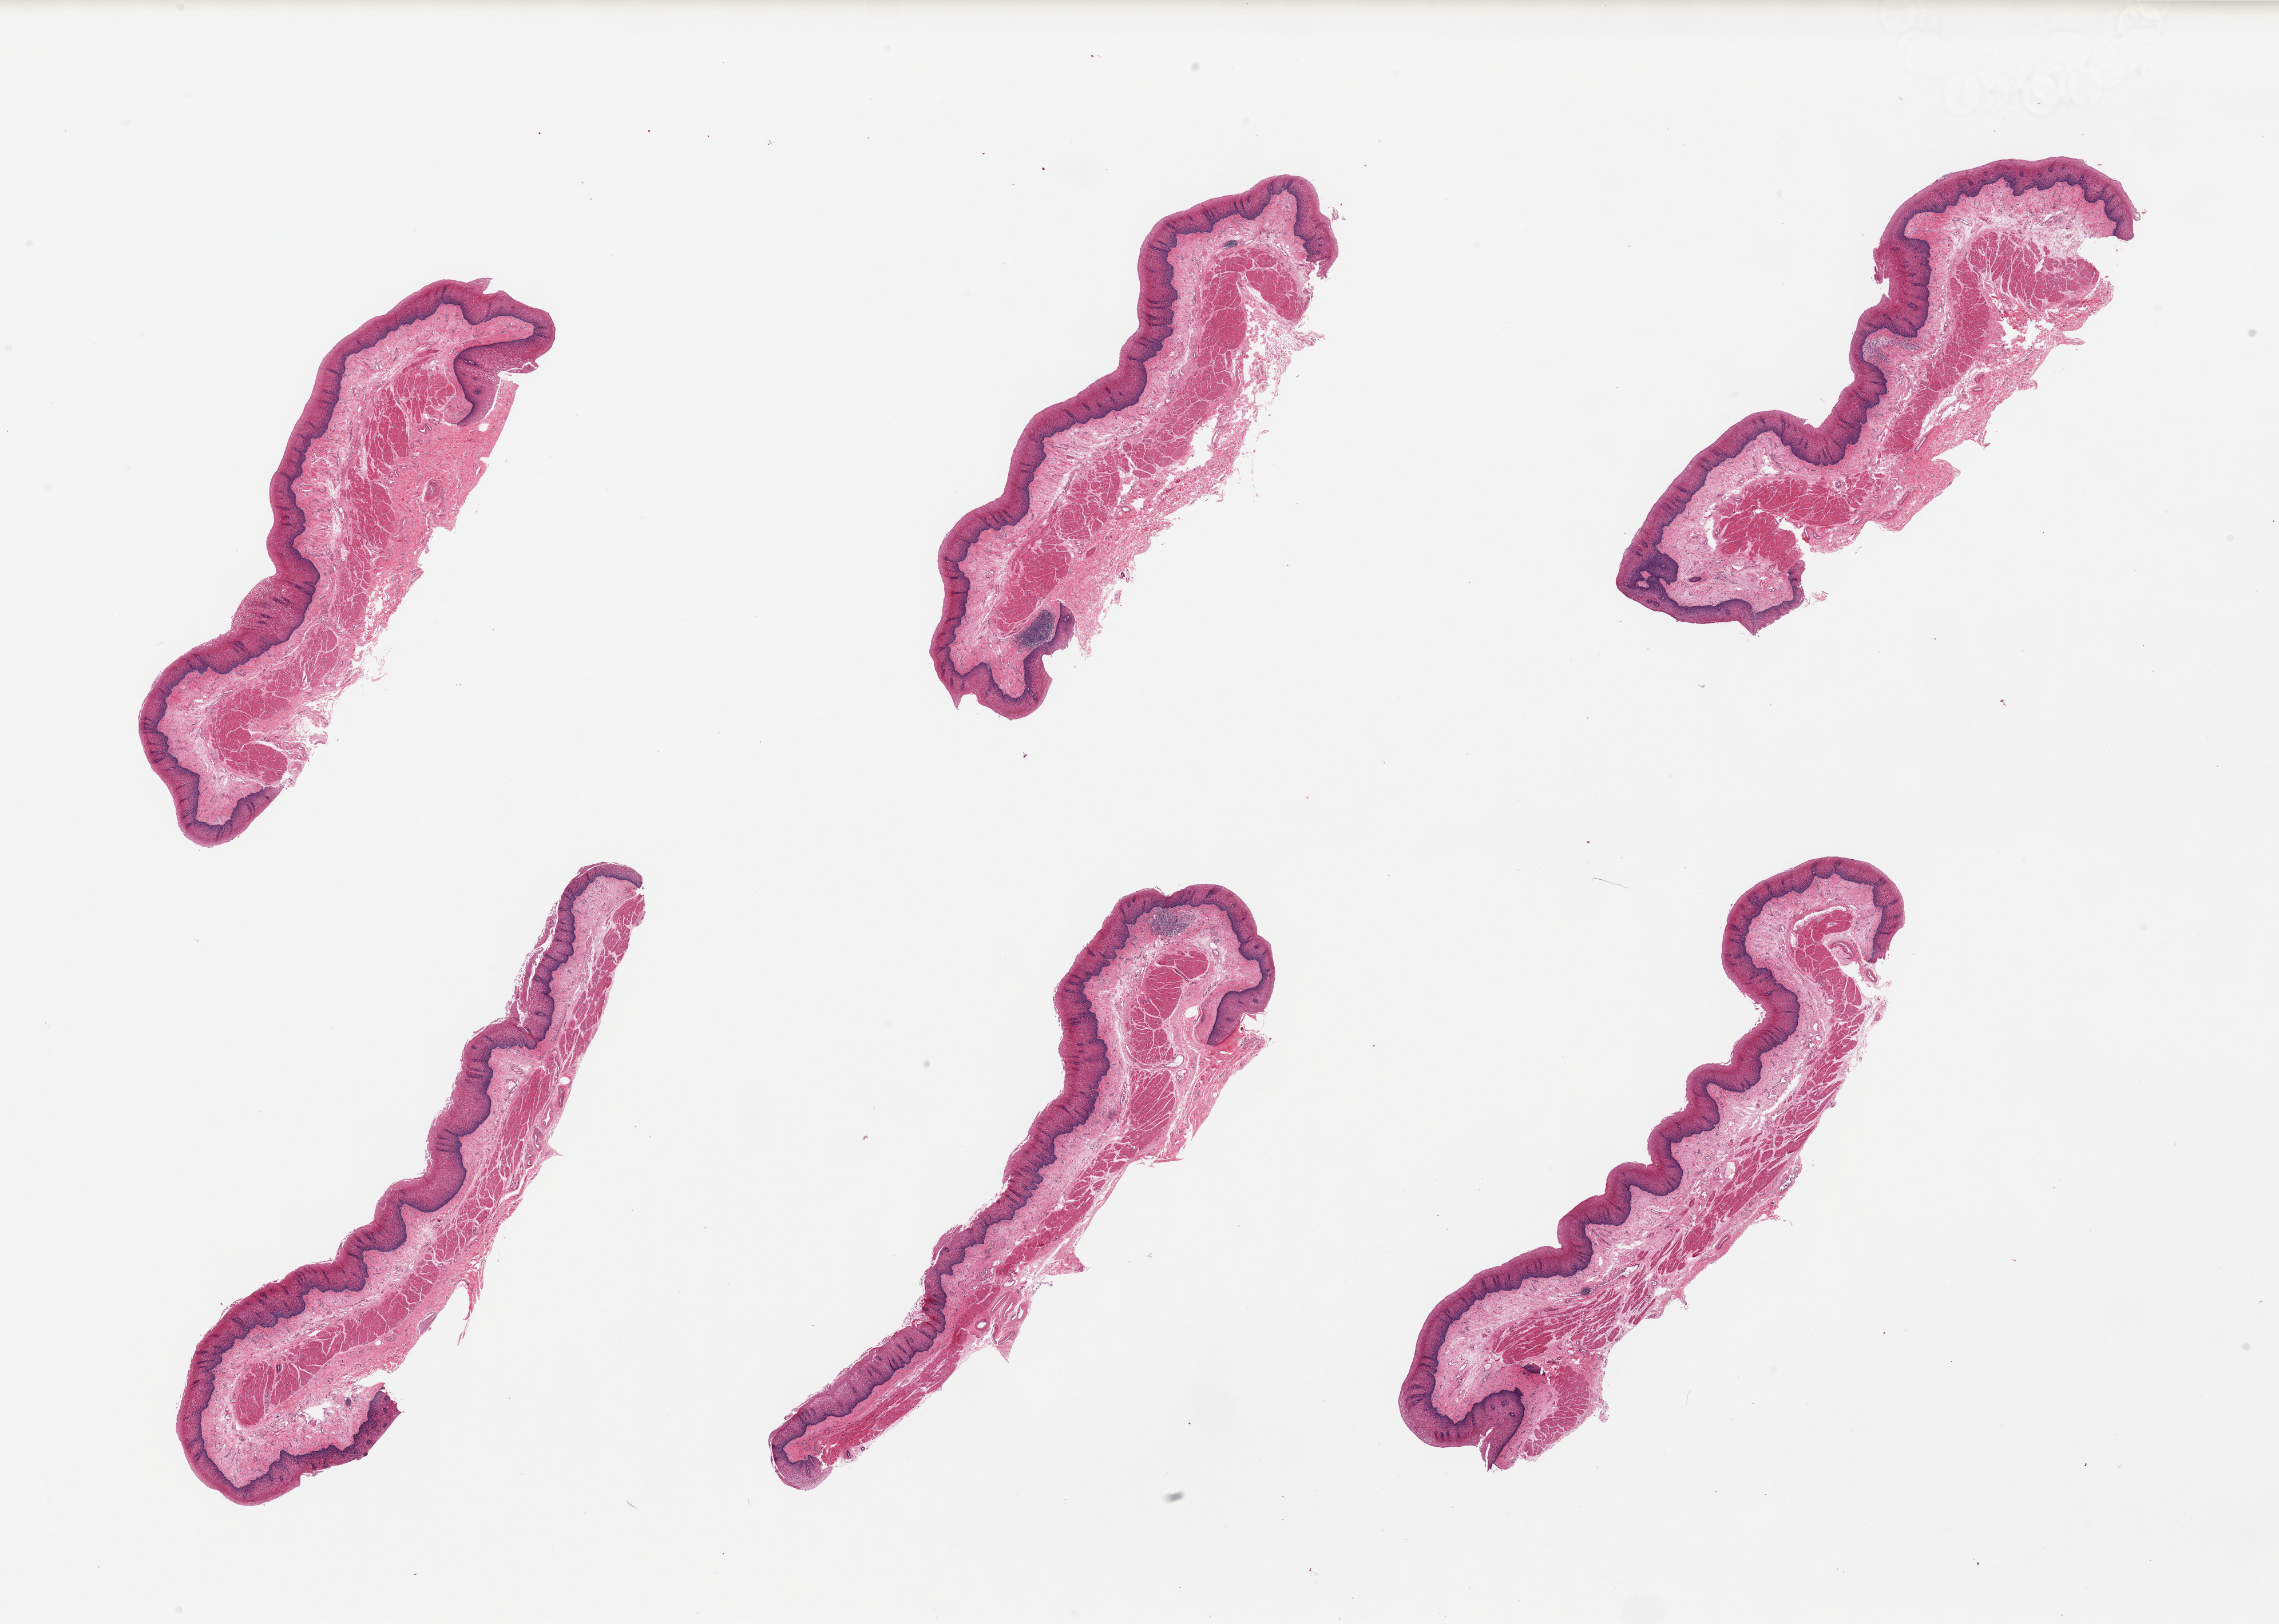
Whole-slide image, hematoxylin and eosin (H&E) stain — low-resolution overview of the scanned area, about 31.5 x 22.5 mm; PAXgene-fixed, paraffin-embedded tissue; section of esophageal mucous membrane (target tissue); donor tissue sample.
Reviewer comment on this tissue sample: 6 pieces. Well dissected mucosa.